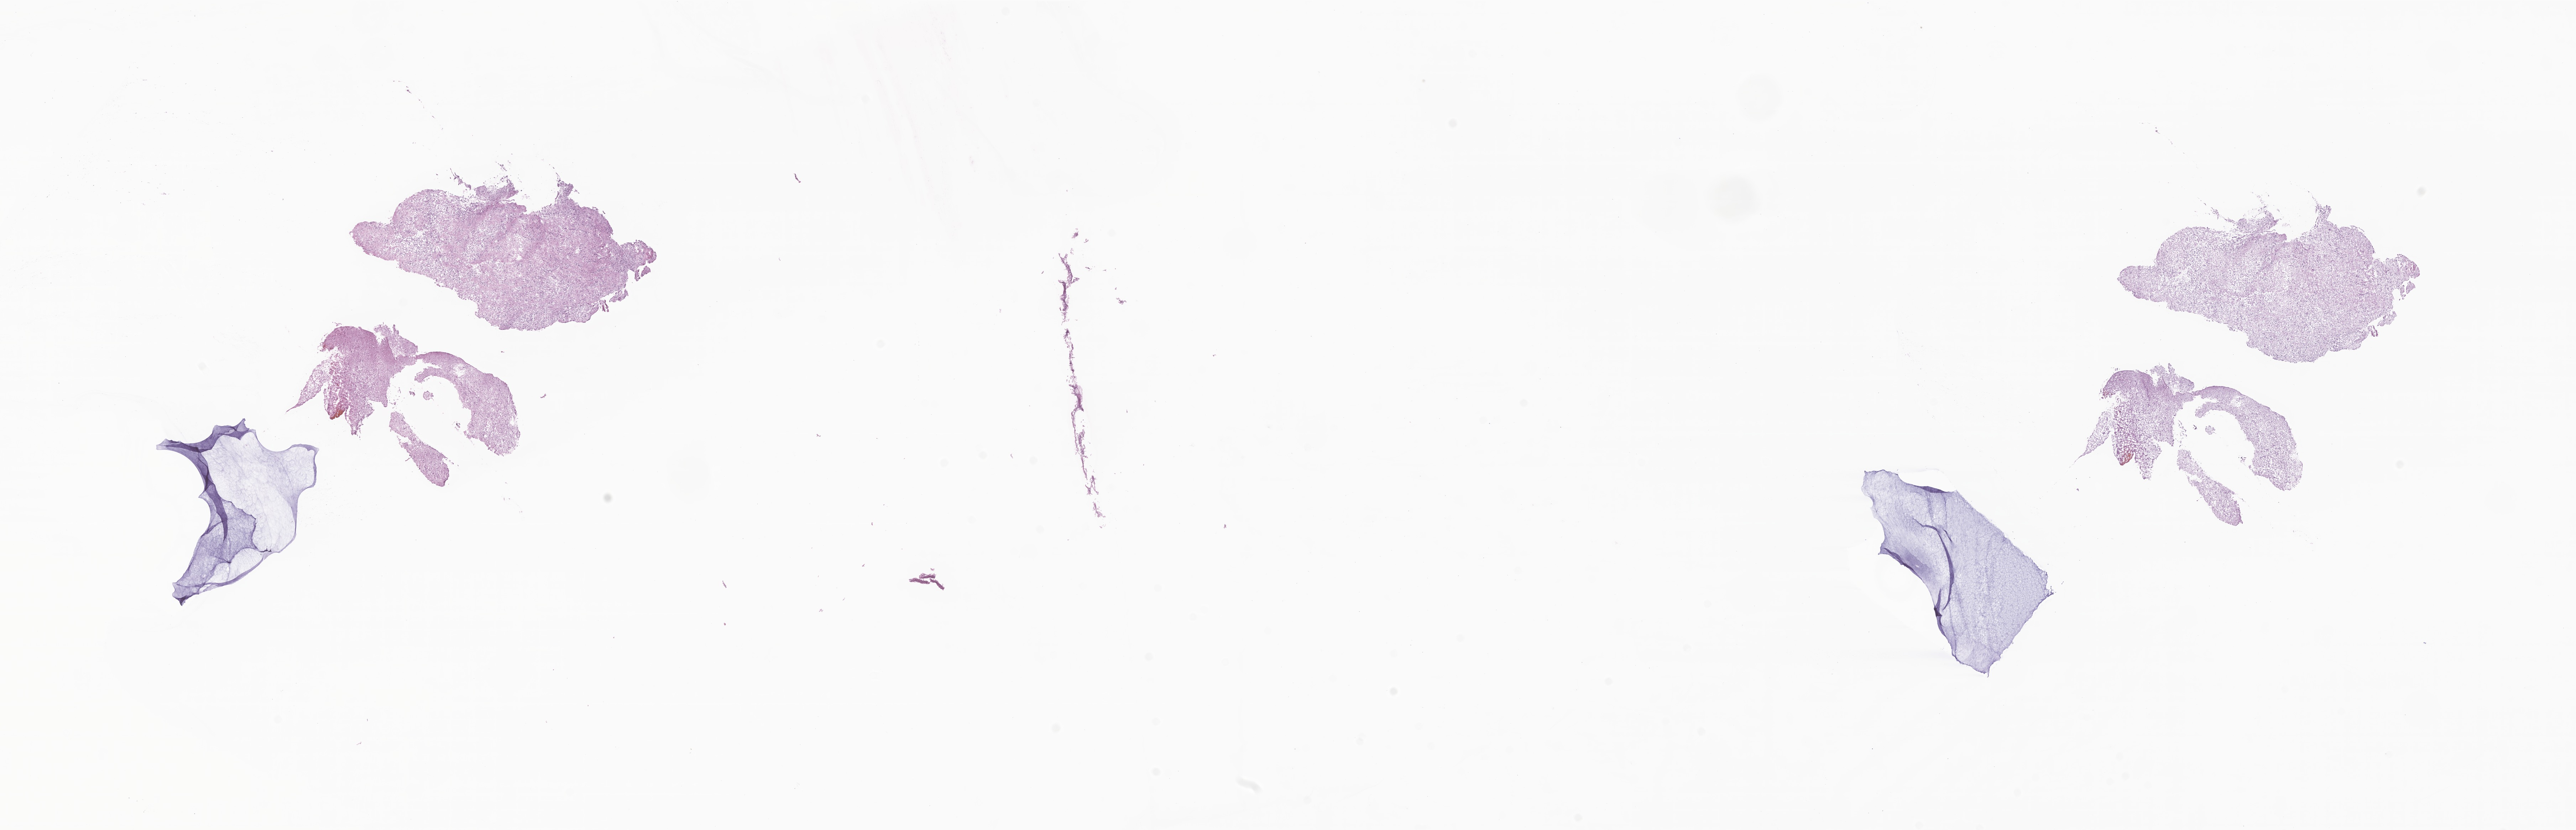
Whole-slide image, haematoxylin and eosin stain of tumor tissue from the brain, whole scanned area (about 30.5 x 9.8 mm) shown as a low-resolution overview, frozen section. Patient: male, age 188 months (15 years 8 months).
Diagnosis (ICD-O-3 morphology term): Ganglioglioma, NOS.